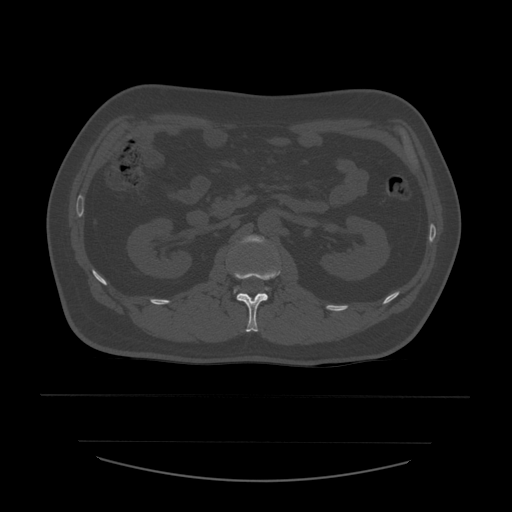
CT including the spine, one axial slice. Slice 217 of 532 in the series (ordered by position). 120 kVp. Bone window (W 1800 / L 400 HU). 1.25 mm slice thickness. 512 × 512 image matrix, field of view 441 × 441 mm. Patient age 44 years. Case-level facts recorded for this patient, not image findings: primary cancer: soft tissue sarcoma.
Structures marked on this image (semi-automatically segmented with operator editing):
- L1 vertebra: box from (x=234, y=266) to (x=281, y=332) px
- L2 vertebra: (x=235, y=236)–(x=269, y=293)